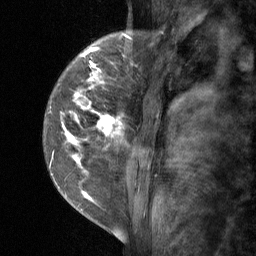
Breast MRI (dynamic contrast-enhanced), one sagittal slice; slice 14 of 64 in the series (ordered by position); dynamic contrast-enhanced study with each time point stored as its own series, time point 2 of 3 at this slice position (early post-contrast, ordered by acquisition time); 1.5 T; TE 4.8 ms, TR 27 ms; 256 × 256 image matrix, field of view 180 × 180 mm. Female patient, age 34 years. Case-level facts recorded for this patient, not image findings: setting: breast cancer imaged before/during neoadjuvant chemotherapy; receptor status: HR-positive, HER2-negative.
Outlined on this slice (semi-automatic segmentation, software-assisted and operator-edited):
- analysis volume of interest (the breast-tissue region the enhancement analysis was run in; not a lesion): bounding box (x1, y1, x2, y2) in pixels: (42, 23, 157, 197)
- tumour enhancement mask (voxels above the 90 % enhancement threshold inside the analysis volume of interest): (50, 34, 153, 197)